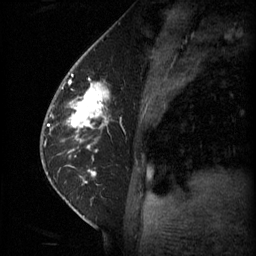
Breast MRI (dynamic contrast-enhanced), one sagittal slice; position 25 of 60 along the scan axis; 3 images stored at this slice position (order not interpretable as contrast timing); 1.5 T; TE 4.2 ms, TR 11 ms; 2 mm slice thickness; 256 × 256 image matrix, field of view 180 × 180 mm. Female patient, age 62 years.
Outlined on this slice (semi-automatically segmented with operator editing):
- analysis volume of interest (the breast-tissue region the enhancement analysis was run in; not a lesion): bounding box [x1, y1, x2, y2] px = [55, 72, 111, 133]
- tumour enhancement mask (voxels above the 70 % enhancement threshold inside the analysis volume of interest): [63, 84, 109, 127]